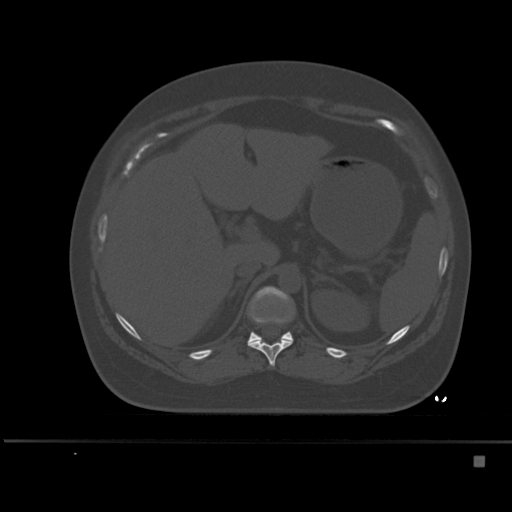
CT including the spine, one axial slice. Slice 224 of 495 in the series (ordered by position). Bone window (W 1800 / L 400 HU). 512 × 512 image matrix, field of view 404 × 404 mm. Female patient, age 33 years. From the clinical record (not read from this slice): primary cancer: breast; vertebrae with lytic lesions (as recorded): T1.
Annotated regions visible in this slice (semi-automatic segmentation, software-assisted and operator-edited):
- T11 vertebra: bounding box (x1, y1, x2, y2) in pixels: (248, 322, 293, 366)
- T12 vertebra: (248, 286, 293, 343)